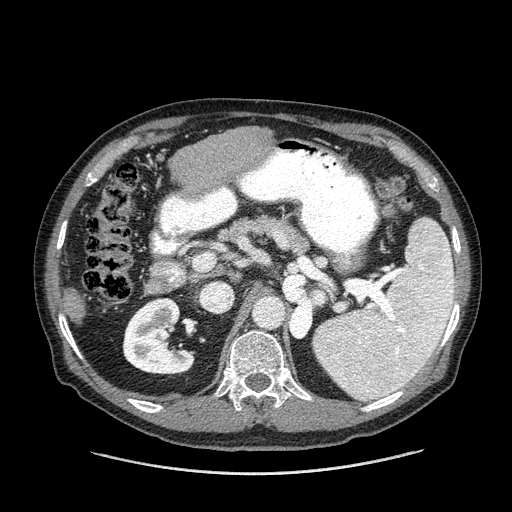
Contrast-enhanced abdominal CT (liver protocol), one axial slice; position 66 of 180 along the scan axis; one of 2 acquisitions stored at this slice position; soft-tissue window (W 400 / L 40 HU); 2.5 mm slice thickness; 512 × 512 image matrix. Case-level facts recorded for this patient, not image findings: diagnosis: hepatocellular carcinoma (patient treated with transarterial chemoembolisation; whether this scan precedes or follows treatment is not stated here); TNM stage (as recorded): Stage-II; Child-Pugh class: A; tumour differentiation: well differentiated; tumour size: 2.8 cm.
Annotated regions visible in this slice (semi-automatically segmented with operator editing):
- liver parenchyma outside the tumour (the mass and vessels are separate outlines, so this box may not span the whole liver): box from (x=62, y=128) to (x=259, y=324) px